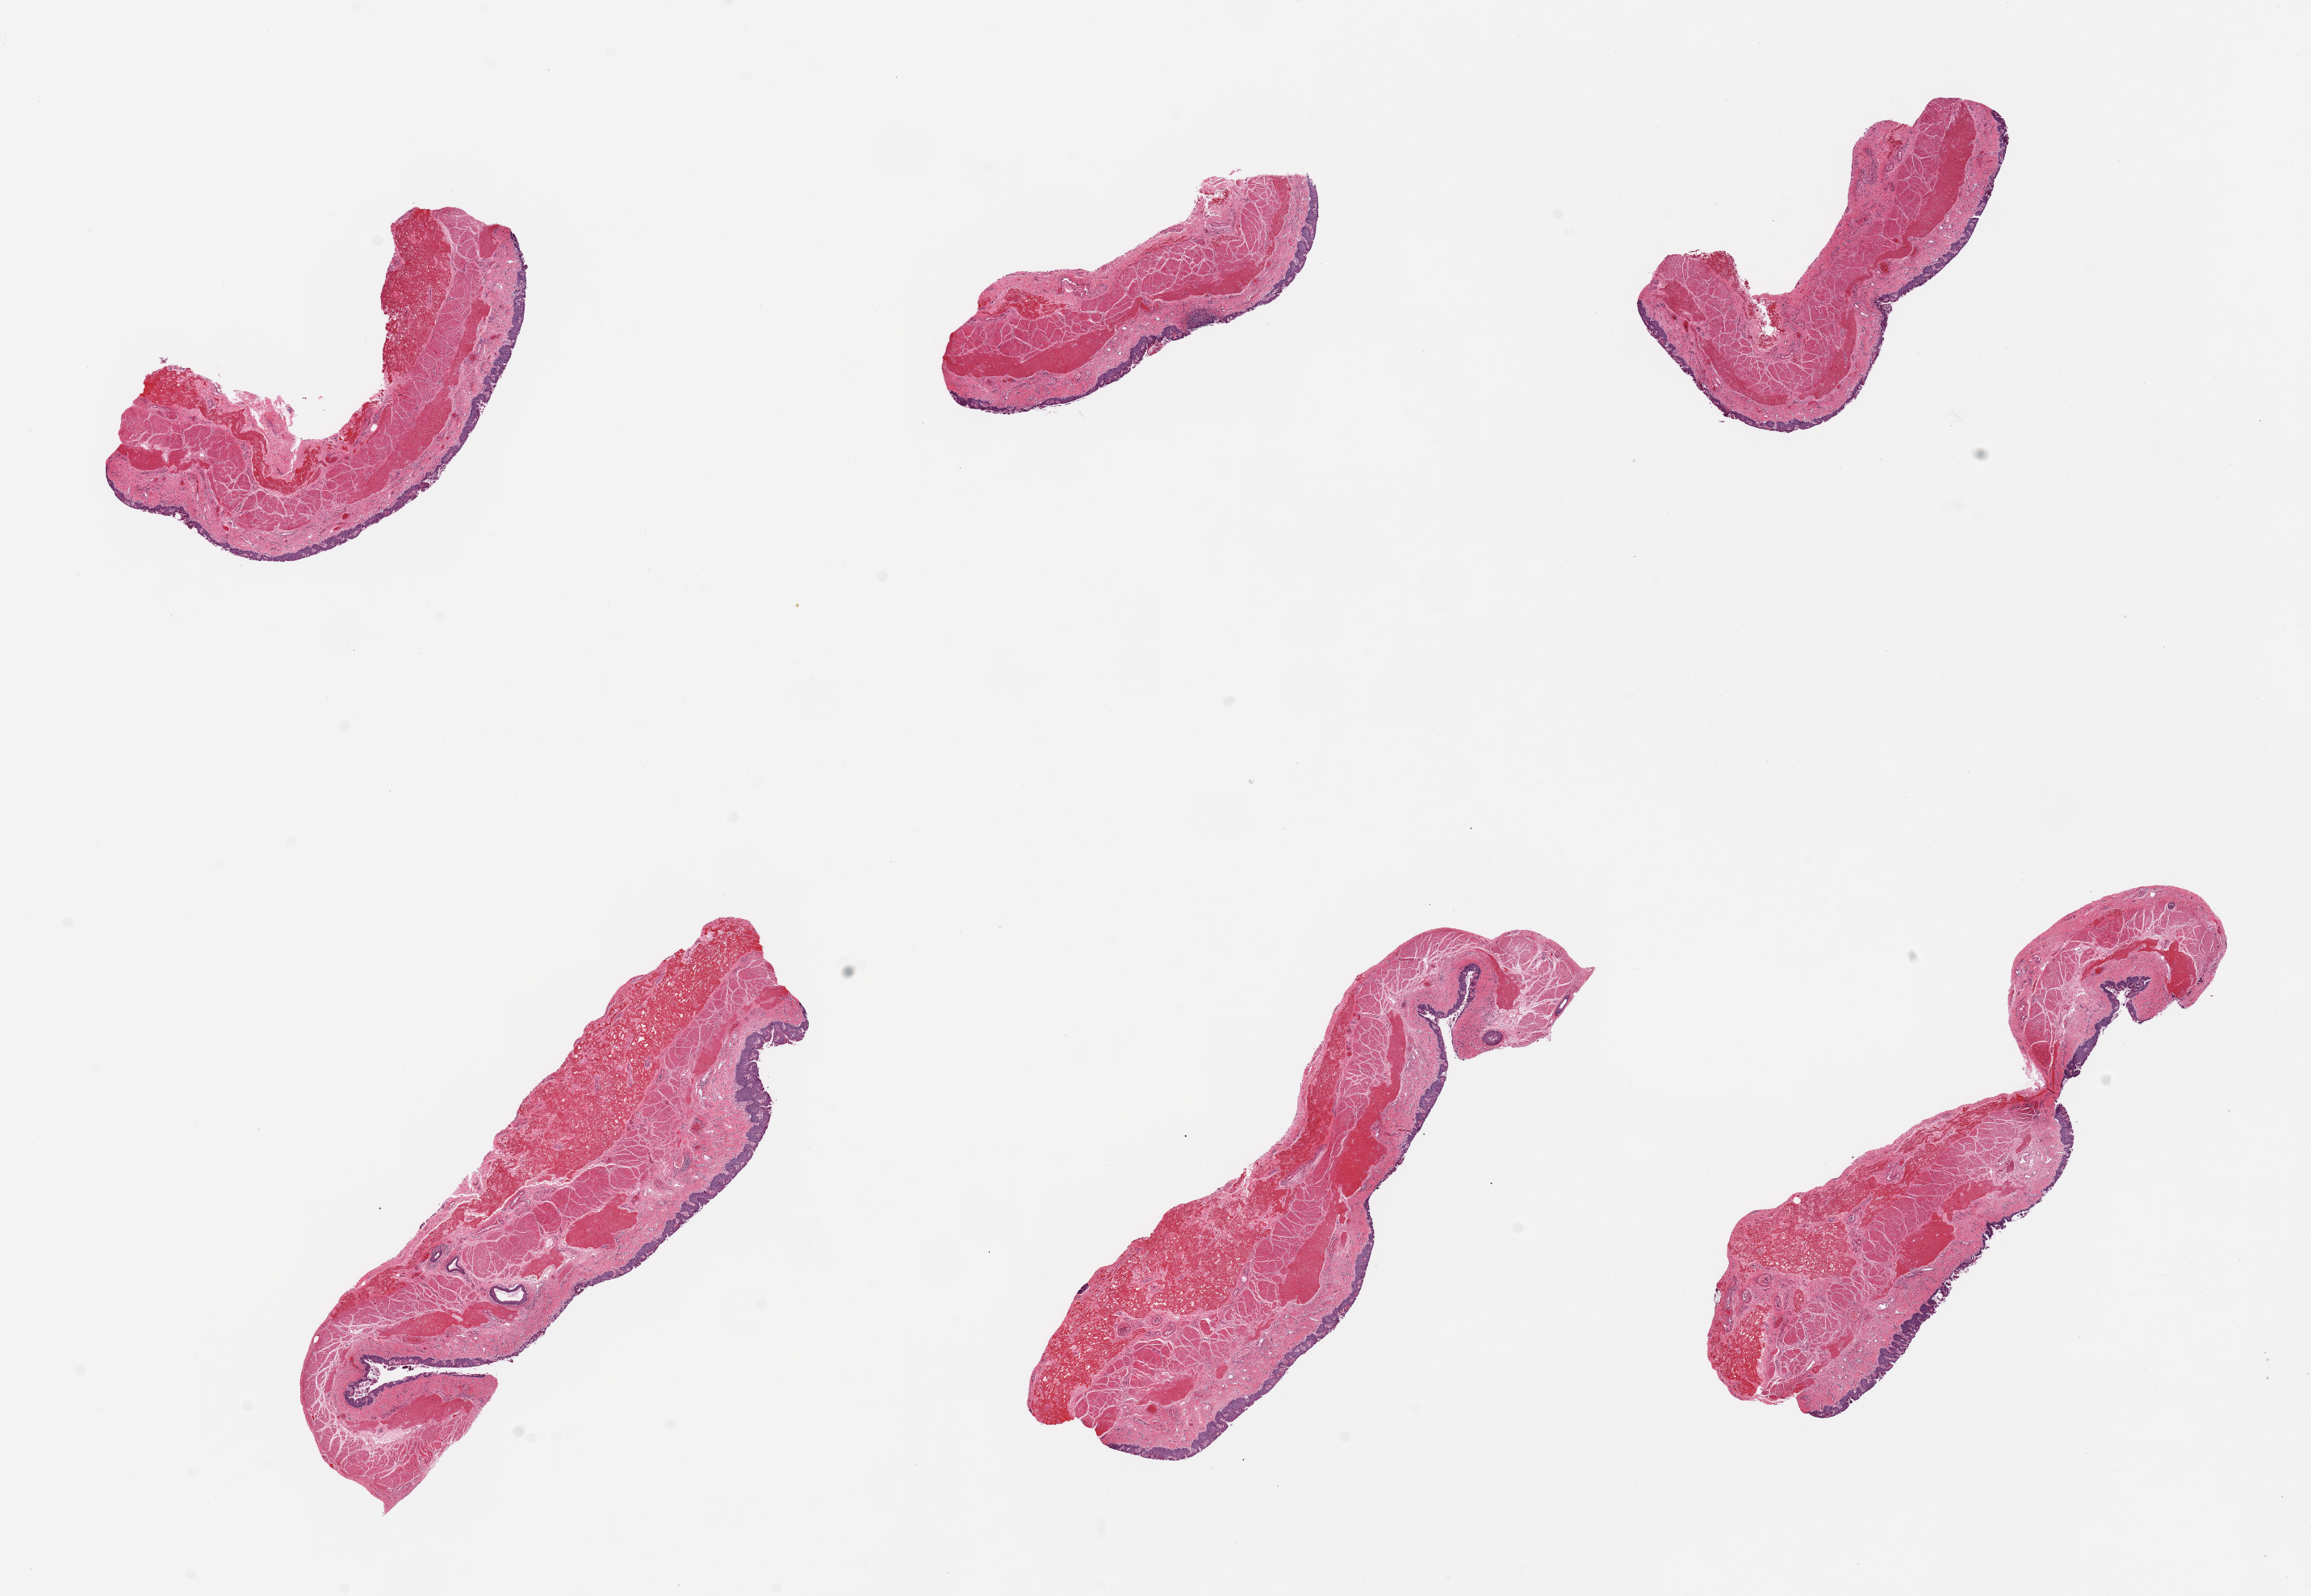
Digitized haematoxylin and eosin-stained section, shown as a low-resolution overview of the whole scanned area (about 22.6 x 15.6 mm), PAXgene-fixed paraffin-embedded (PFPE) section, target tissue: esophageal mucous membrane, tissue donor sample. Donor sex: female.
Review note (as recorded): 6 pieces, squamous mucosa is 5% thickness, sloughed in some areas.